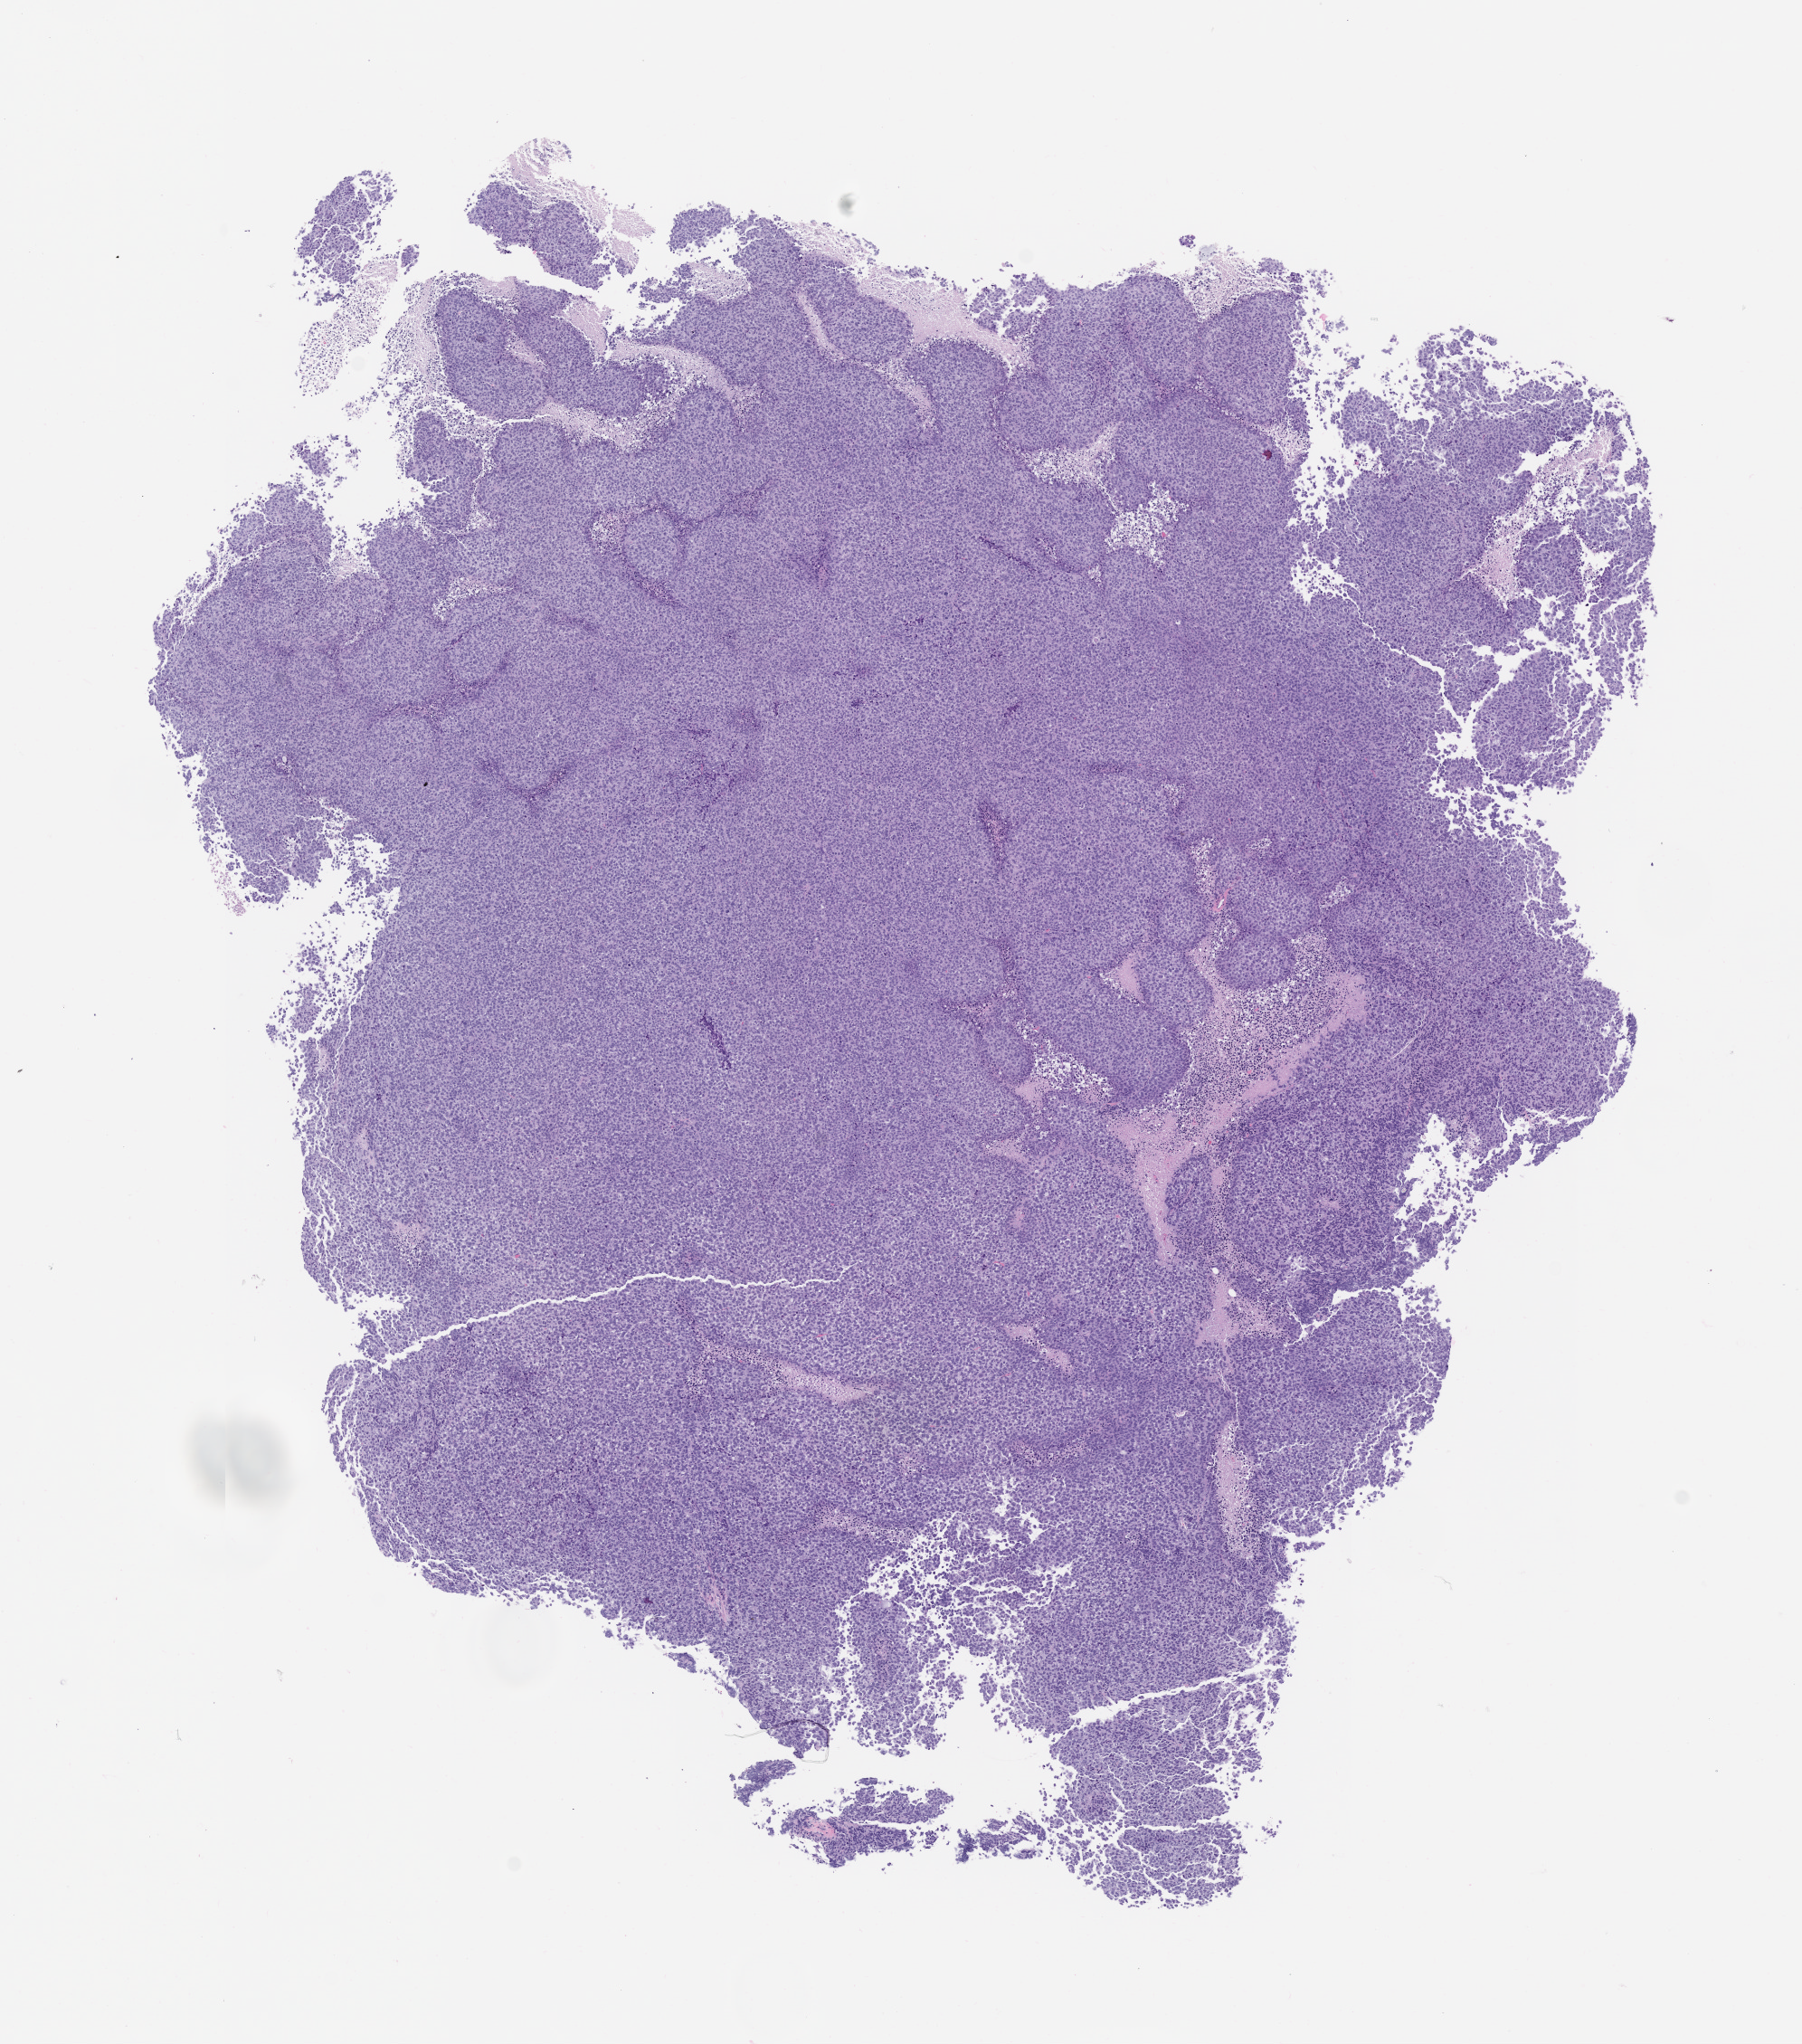
H&E whole-slide image of a patient-derived xenograft (PDX) tumor grown in a mouse, passage 0 — shown as a low-resolution overview of the whole scanned area (about 8.0 x 9.1 mm); FFPE section; originating tumor site category: musculoskeletal.
• originating patient diagnosis: Ewing Sarcoma|Primitive Neuroectodermal Tumor